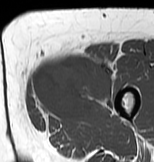
MRI of an extremity soft-tissue mass, one axial slice; slice 22 of 83 in the series (ordered by position); MR volume resampled by the dataset authors to the PET/CT grid (not the native acquisition matrix); 3.27 mm slice thickness; 154 × 162 image matrix, field of view 150 × 158 mm. Female patient. From the clinical record (not read from this slice): histological type: myxofibrosarcoma; grade: intermediate; site of the primary tumour: left thigh.
Structures marked on this image (expert contour drawn on MRI and transferred to this co-registered scan by the dataset authors):
- gross tumour volume including surrounding oedema: bounding box <30,50,116,124> (left, top, right, bottom; pixels)
- gross tumour volume (mass): <33,55,114,120>